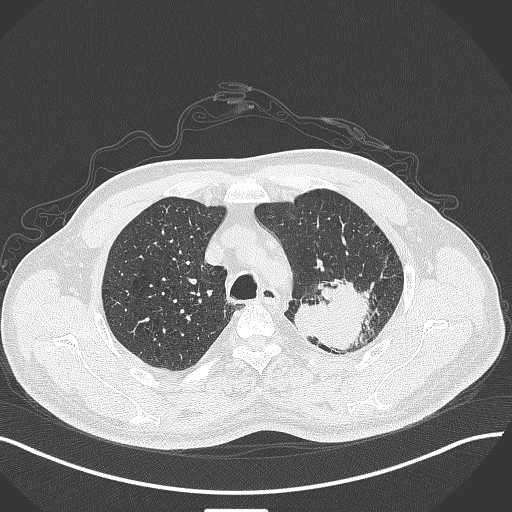
Chest CT, one axial slice. Slice 331 of 429 in the series (ordered by position). Reconstruction kernel B70f. 120 kVp. Lung window (W 1500 / L -600 HU). 512 × 512 image matrix, field of view 400 × 400 mm. Patient: male, 55 years. From the clinical record (not read from this slice): clinical TNM (as recorded): T3 N0 M1c.
Annotated regions visible in this slice (bounding box drawn by a radiologist):
- lung tumour (recorded histology: adenocarcinoma): bounding box <289,278,374,358> (left, top, right, bottom; pixels)